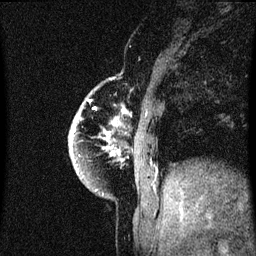
Breast MRI (dynamic contrast-enhanced), one sagittal slice. Position 10 of 60 along the scan axis. Dynamic contrast-enhanced series, image 2 of 3 at this slice position (ordered by acquisition). 1.5 T. TE 4.2 ms, TR 8.4 ms. 2 mm slice thickness. 256 × 256 image matrix. Female patient, age 60 years.
Structures marked on this image (semi-automatically segmented with operator editing):
- analysis volume of interest (the breast-tissue region the enhancement analysis was run in; not a lesion): box from (x=70, y=94) to (x=123, y=195) px
- tumour enhancement mask (voxels above the 70 % enhancement threshold inside the analysis volume of interest): (x=70, y=116)–(x=115, y=171)